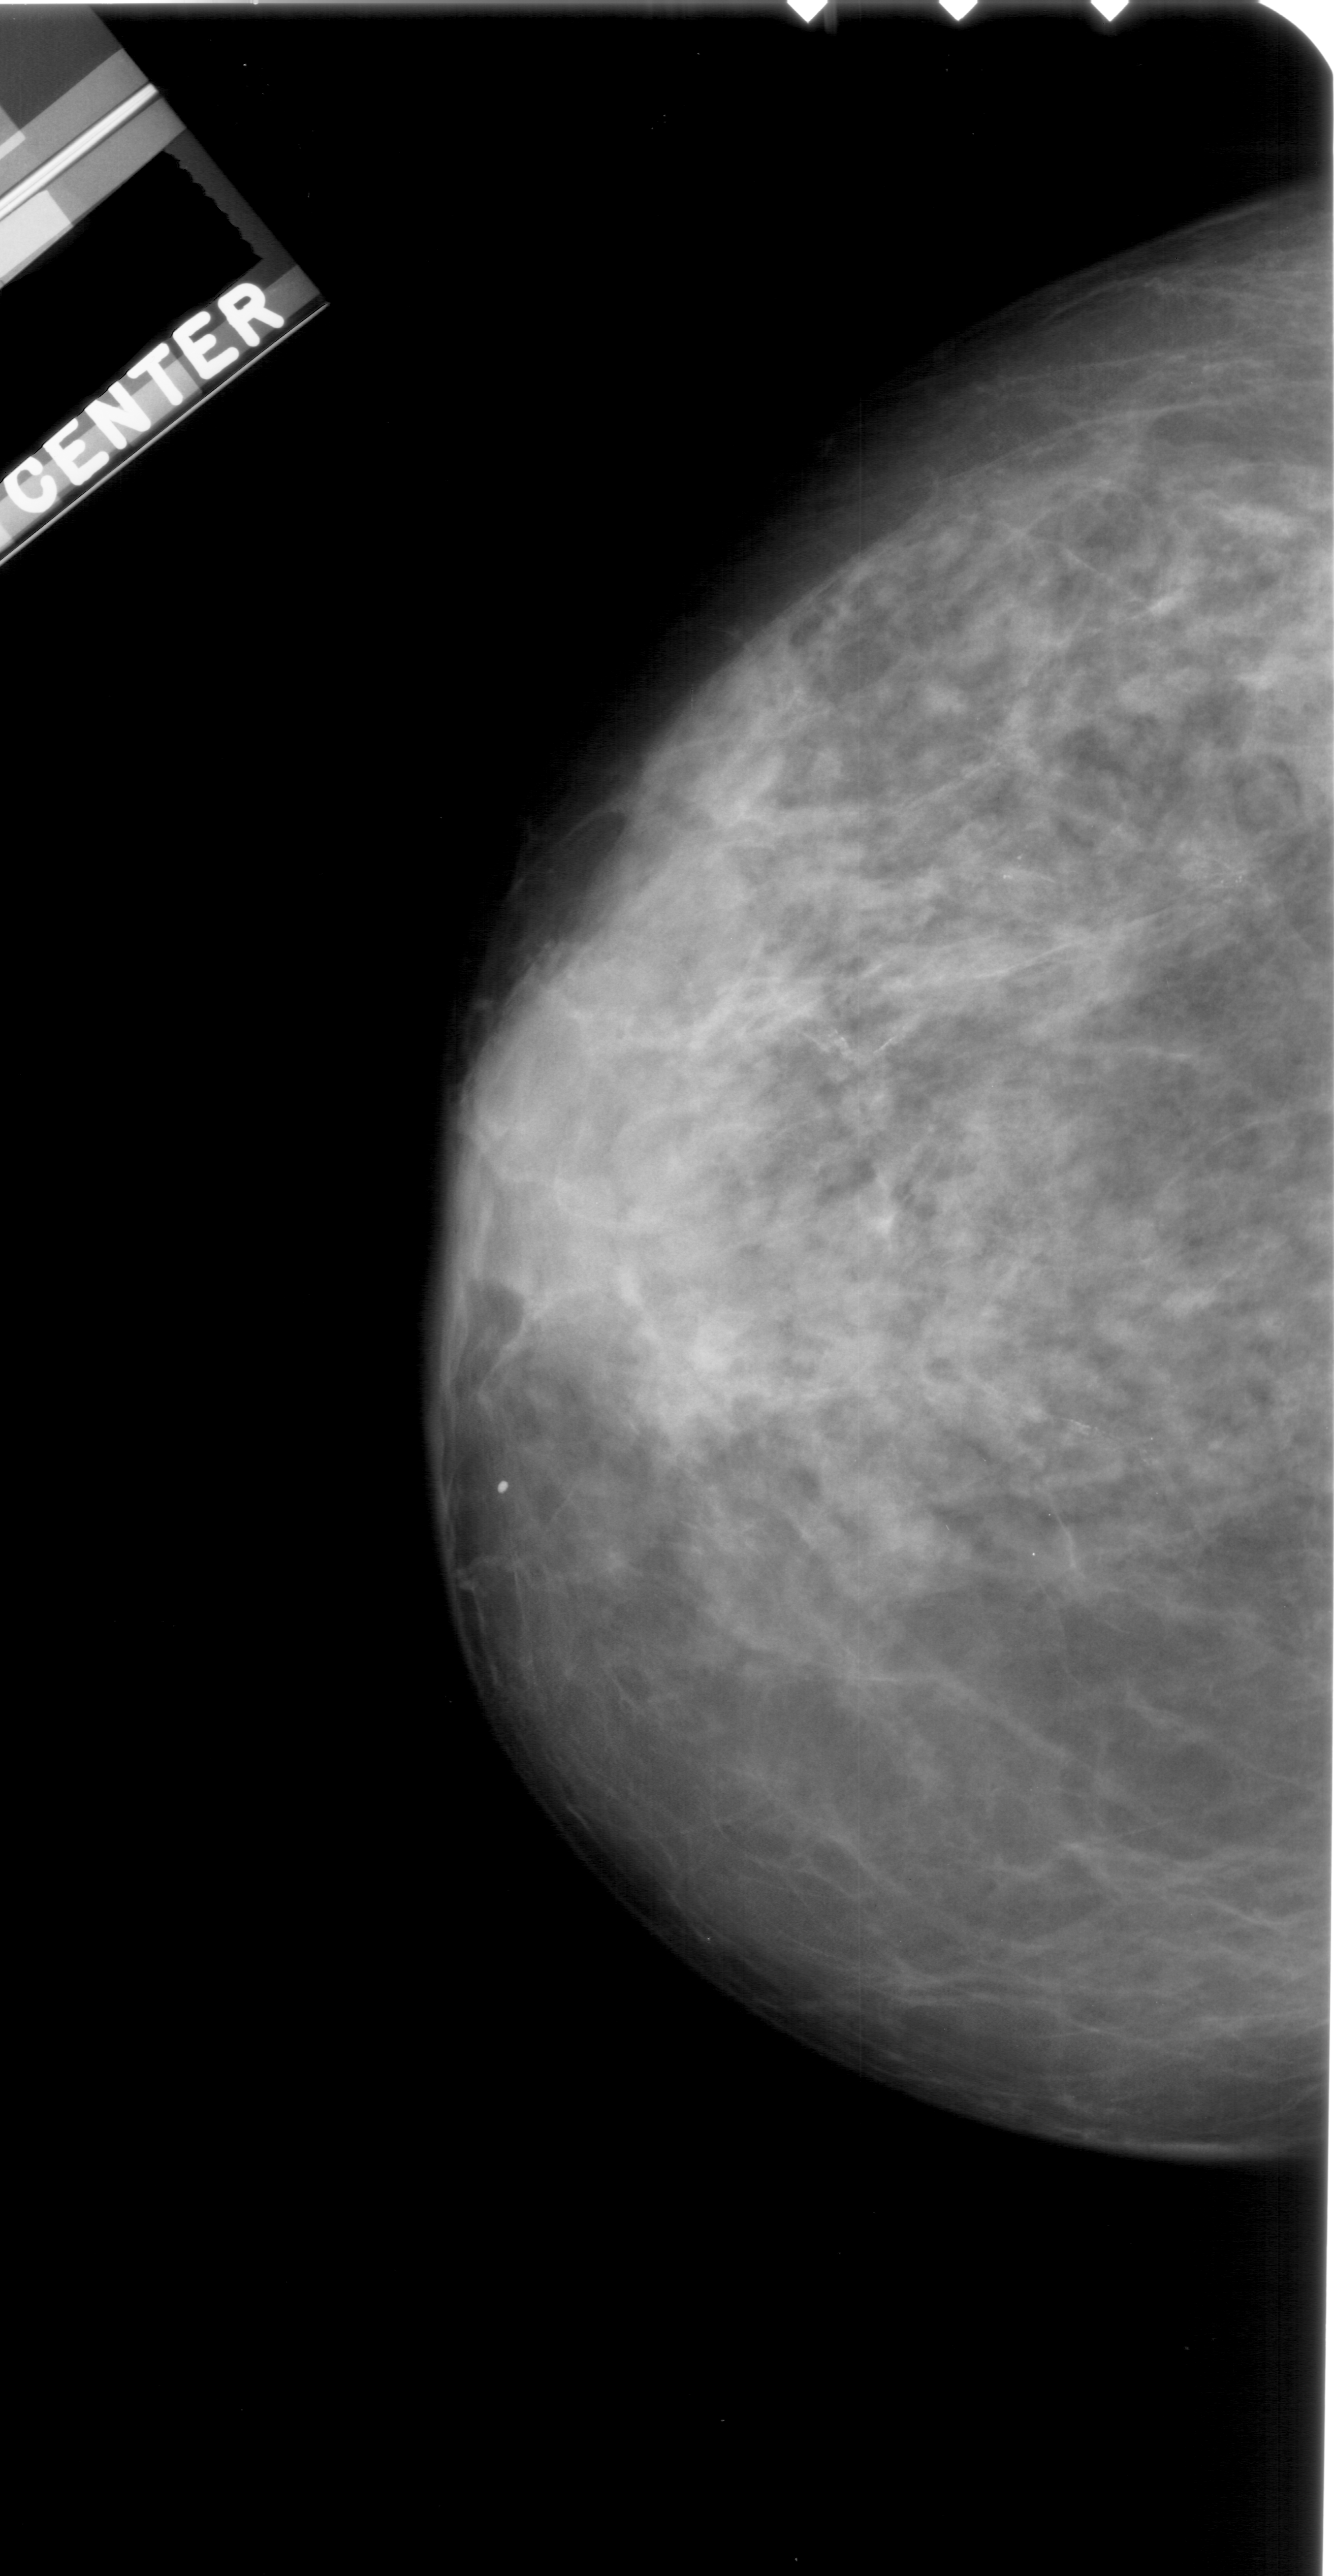
Mammogram (digitized film); left breast; CC view; breast composition: heterogeneously dense (BI-RADS density category 3 of 4).
- Abnormality record for this image: calcifications, morphology pleomorphic, distribution segmental; BI-RADS assessment category 4; subtlety rating 2 on a 1 (subtle) to 5 (obvious) scale; pathology (as recorded): malignant.